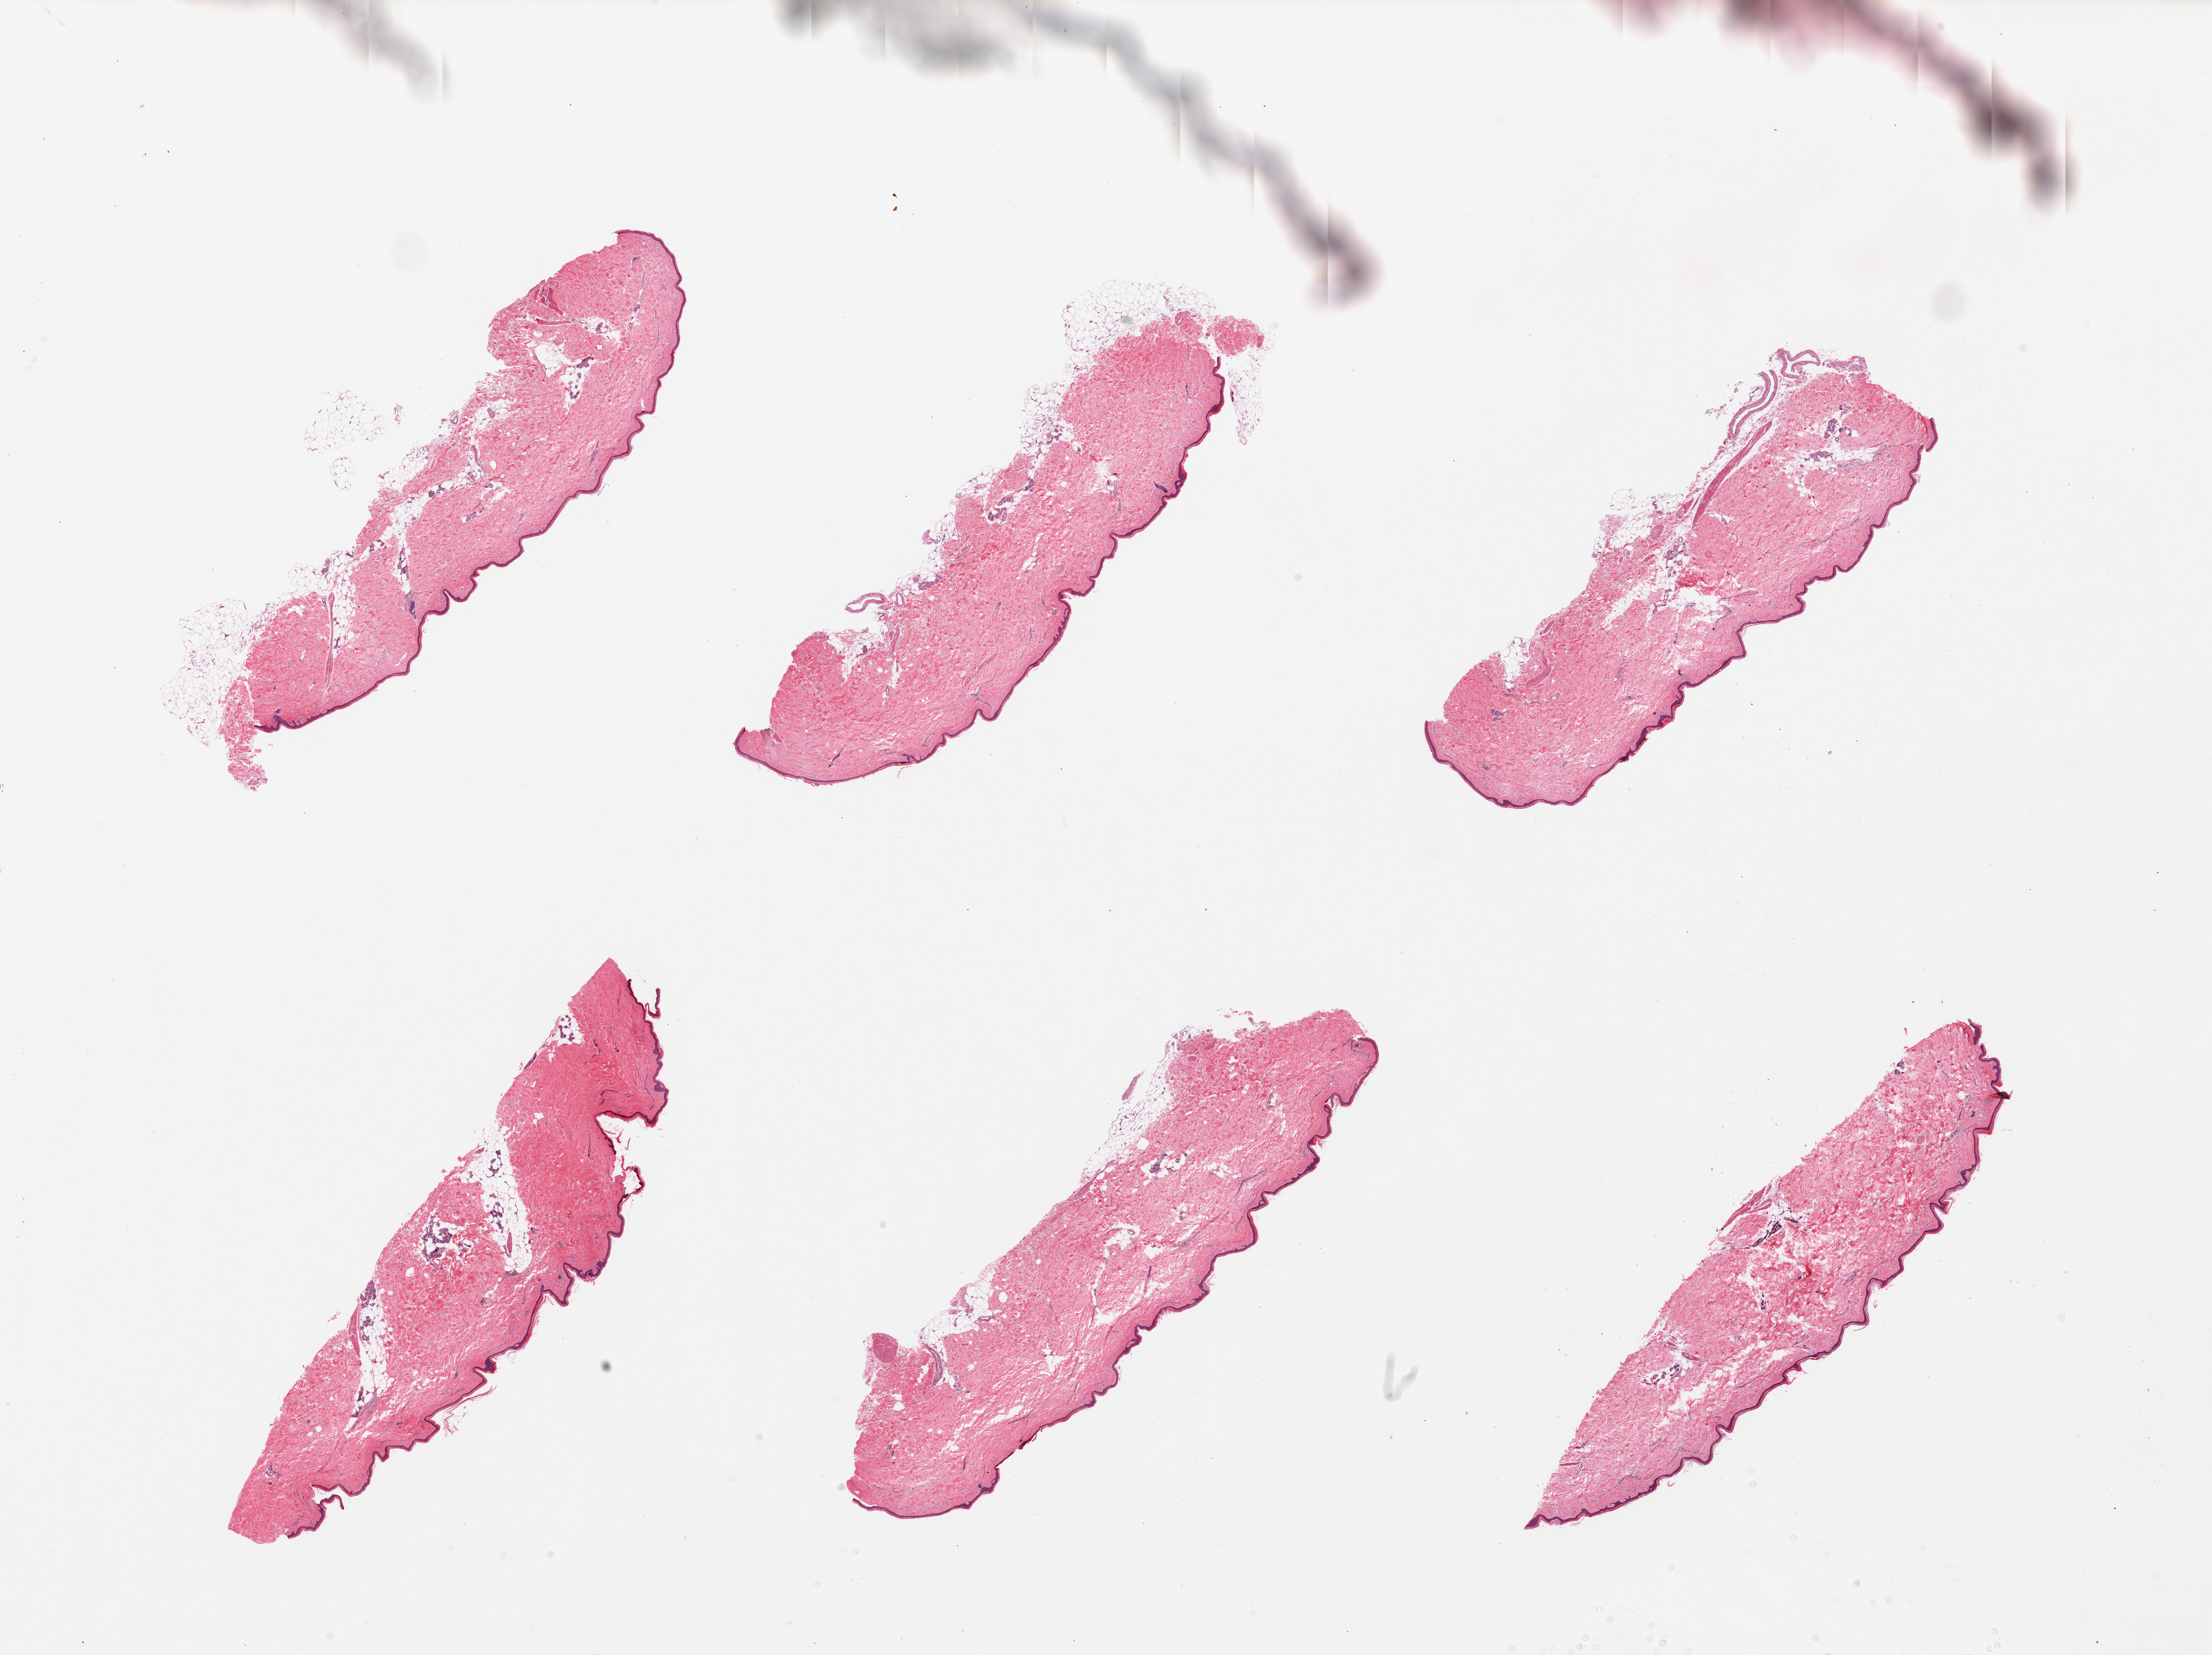
Whole-slide image, haematoxylin and eosin stain — shown as a low-resolution overview of the whole scanned area (about 29.5 x 22.1 mm, acquisition: 20x scan). PAXgene-fixed paraffin-embedded (PFPE) section. Section of skin of lower leg (target tissue). Tissue donor sample. Donor sex: male.
Review note (as recorded): 6 pieces, relatively well trimmed with <10% attached/internal fat, squamous epithelium measures 26 to 30 microns.